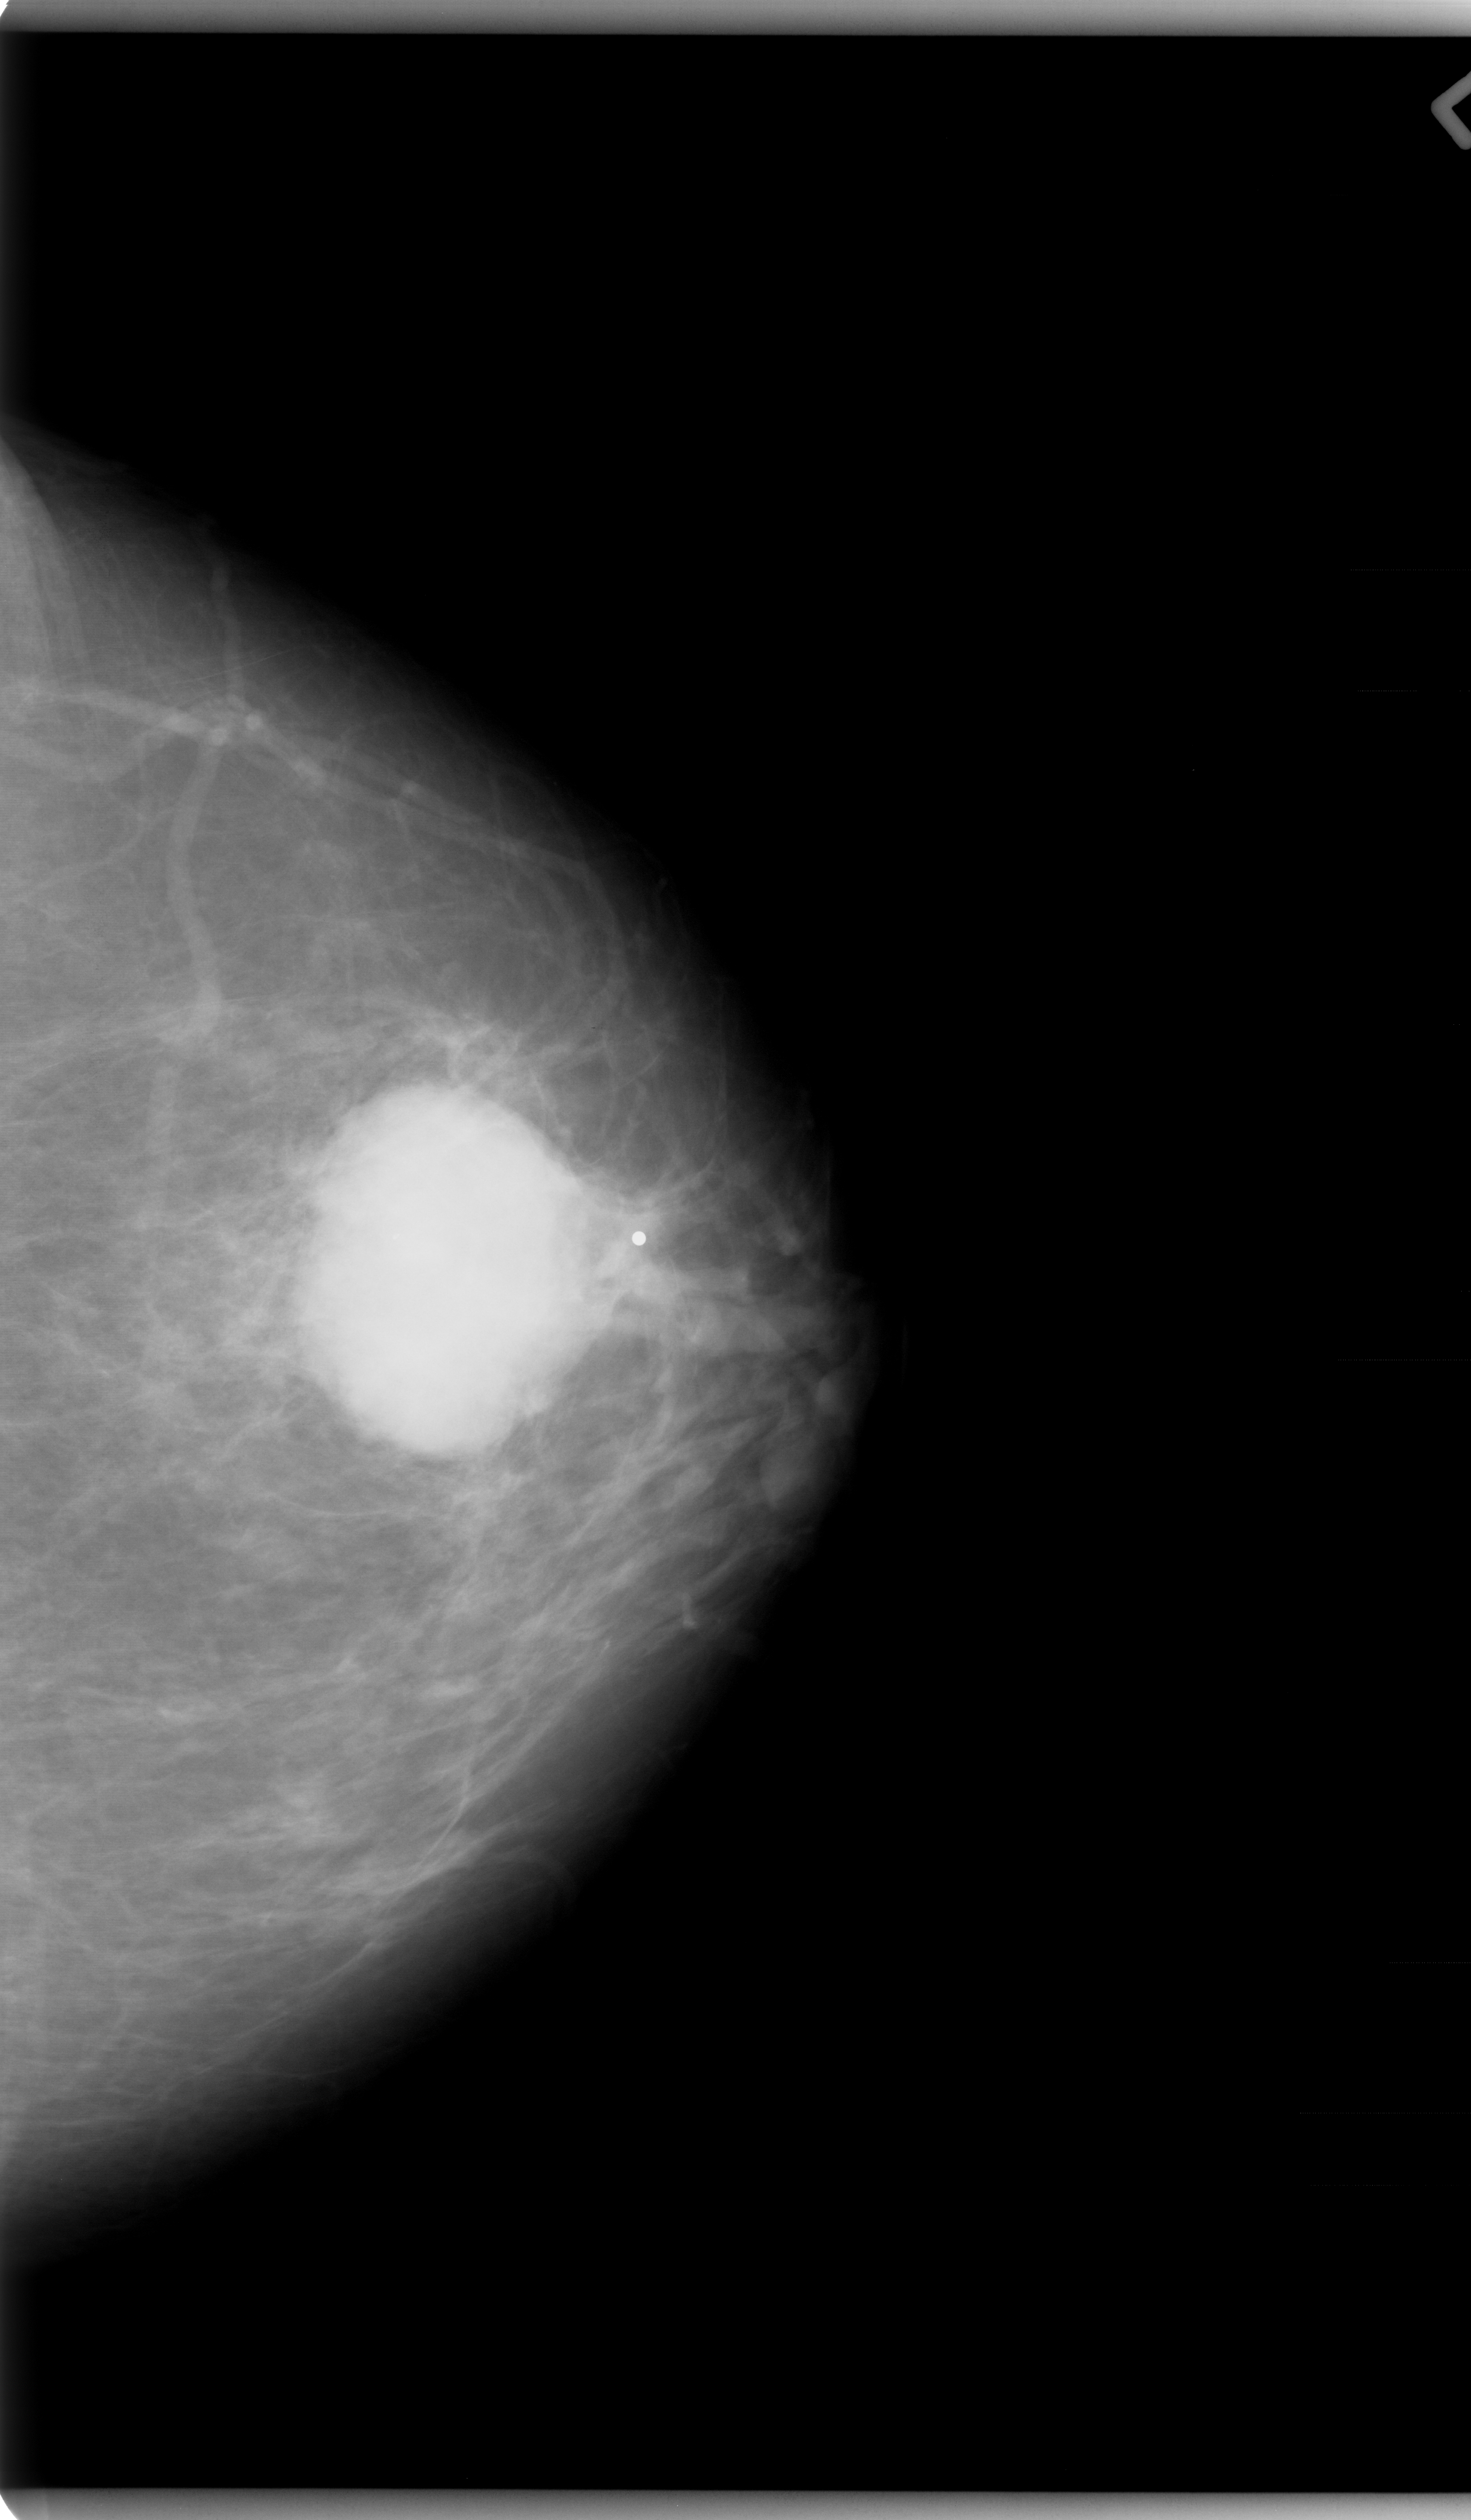
Digitized screen-film mammogram, left breast, CC view, breast composition: scattered fibroglandular densities (BI-RADS density category 2 of 4).
Marked abnormality: mass, shape oval, margins microlobulated; BI-RADS assessment category 5; pathology result (as recorded, not read from the image): malignant.